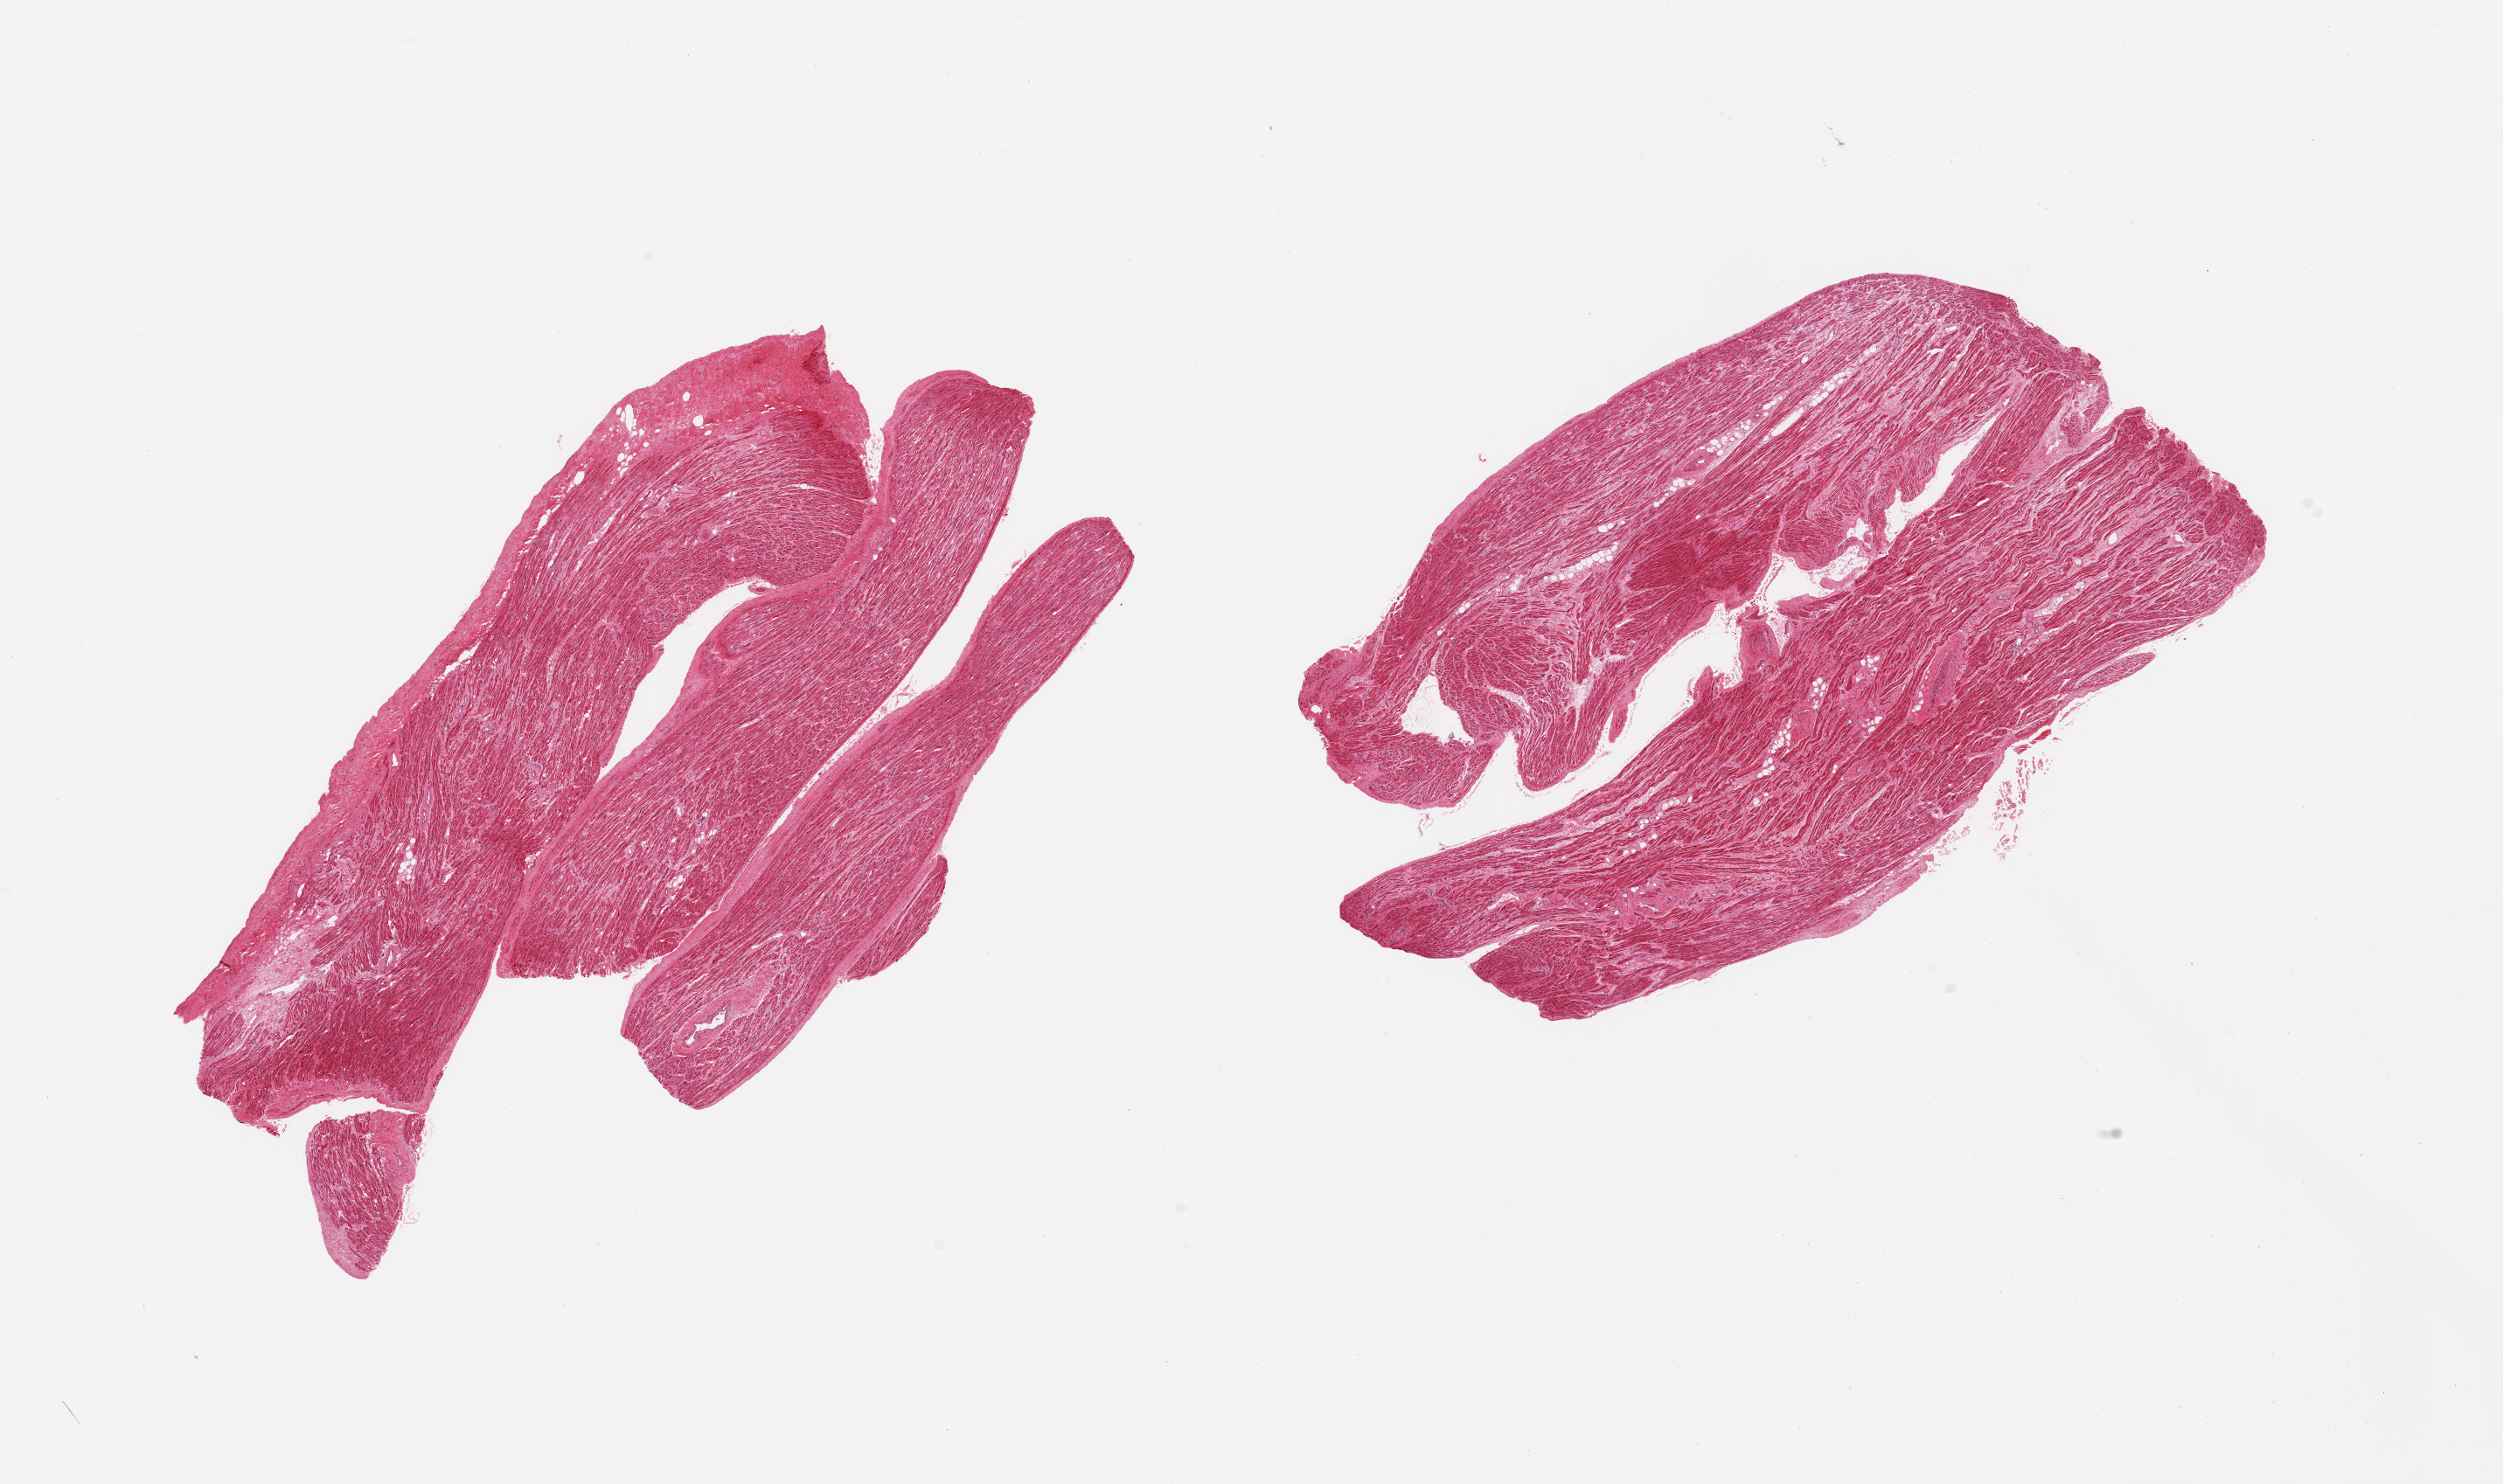
Digitized hematoxylin and eosin (H&E)-stained section, brightfield, shown as a low-resolution overview of the whole scanned area (about 22.6 x 13.4 mm, acquisition: 20x scan); PAXgene-fixed, paraffin-embedded tissue; target tissue: auricular appendage; tissue donor sample. Male donor.
- review note (as recorded): 2 pieces; includes trivial fat